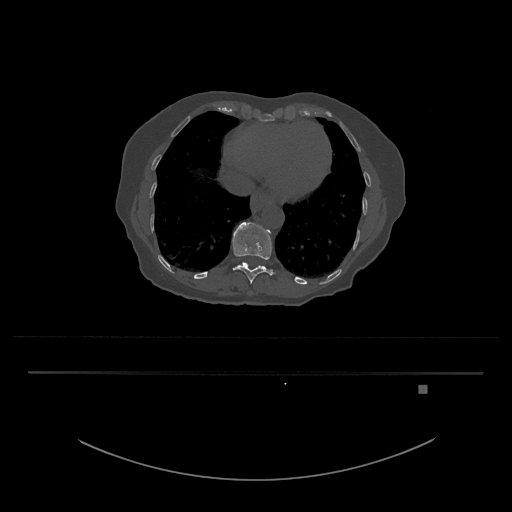
CT including the spine, one axial slice; slice 660 of 797 in the series (ordered by position); 120 kVp; bone window (W 1800 / L 400 HU); 0.5 mm slice thickness; 512 × 512 image matrix. Female patient, age 57 years. Case-level facts recorded for this patient, not image findings: primary cancer: cervical.
Annotated regions visible in this slice (semi-automatic segmentation, software-assisted and operator-edited):
- T11 vertebra: bounding box [x1, y1, x2, y2] px = [232, 222, 274, 284]
- T12 vertebra: [238, 262, 265, 268]